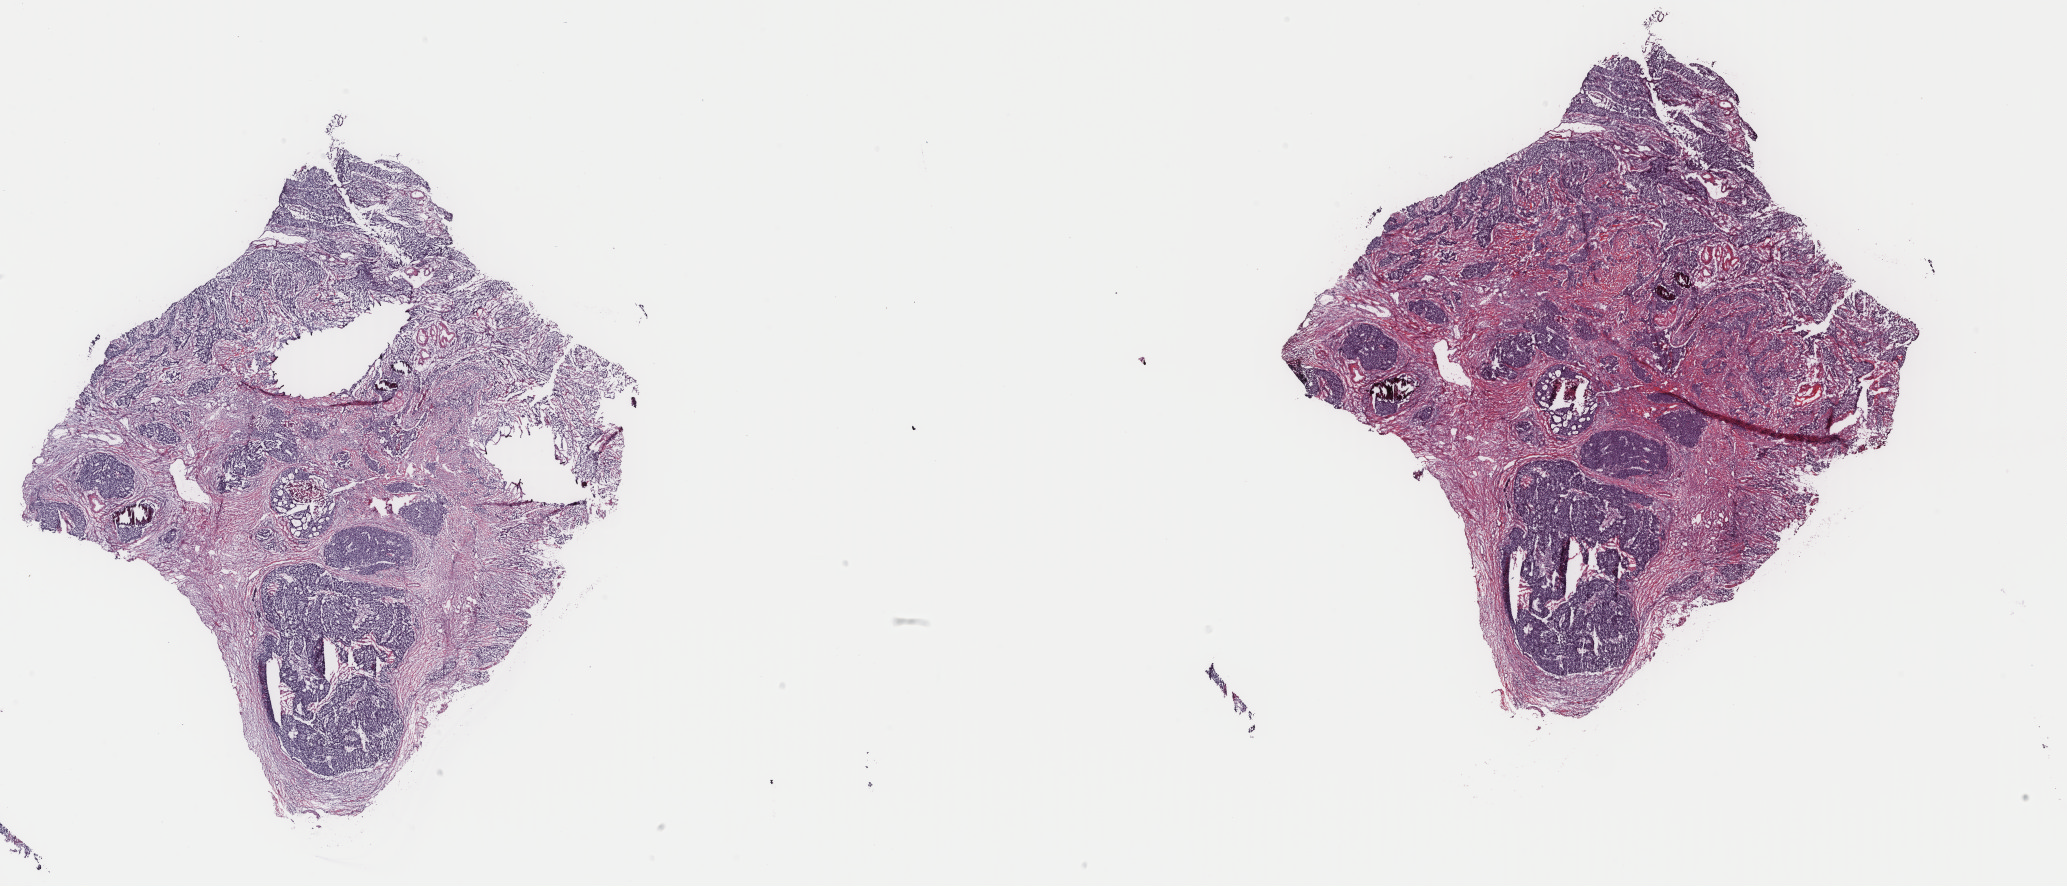
Whole-slide histology image, H&E — low-resolution overview of the scanned area, about 32.8 x 14.1 mm (acquisition: 40x scan), frozen section from the top of the tissue portion, cervix, primary tumour sample. Female, age 50 years at initial diagnosis. Histologic grade: G3 (poorly differentiated). Composition of this section per pathologist review: tumour cells 95%, tumour nuclei 65%, normal cells 0%, stromal cells 0%, necrosis 5%. Infiltration values recorded for this section: lymphocyte infiltration 5%, monocyte infiltration 0%, neutrophil infiltration 0%.
* pathologic diagnosis: Squamous cell carcinoma, NOS (cervix uteri)
* FIGO stage: IIA1